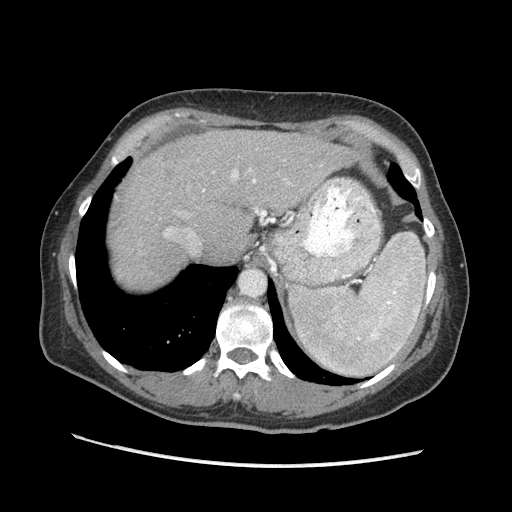
Contrast-enhanced abdominal CT (liver protocol), one axial slice. Position 147 of 170 along the scan axis. 140 kVp. Soft-tissue window (W 400 / L 40 HU). 2.5 mm slice thickness. 512 × 512 image matrix. From the clinical record (not read from this slice): diagnosis: hepatocellular carcinoma (patient treated with transarterial chemoembolisation; whether this scan precedes or follows treatment is not stated here); TNM stage (as recorded): Stage-II; Child-Pugh class: A; tumour differentiation: no biopsy; tumour nodularity: multinodular.
Outlined on this slice (semi-automatically segmented with operator editing):
- abdominal aorta: bounding box (x1, y1, x2, y2) in pixels: (240, 269, 264, 295)
- liver parenchyma outside the tumour (the mass and vessels are separate outlines, so this box may not span the whole liver): (112, 130, 370, 288)
- liver vessels: (164, 168, 290, 237)